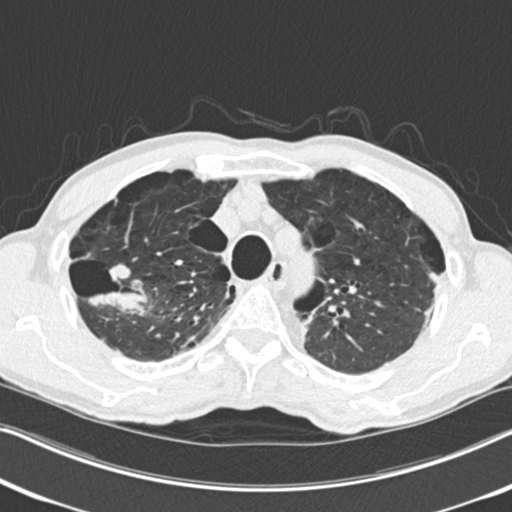
Low-dose screening chest CT, one axial slice. Slice 196 of 251 in the series (ordered by position). Reconstruction kernel B30f. Lung window (W 1500 / L -600 HU). 2 mm slice thickness. 512 × 512 image matrix.
Annotated regions visible in this slice (expert manual segmentation):
- lesion 1 (tumor, upper lobe of right lung): bounding box <89,264,148,314> (left, top, right, bottom; pixels)